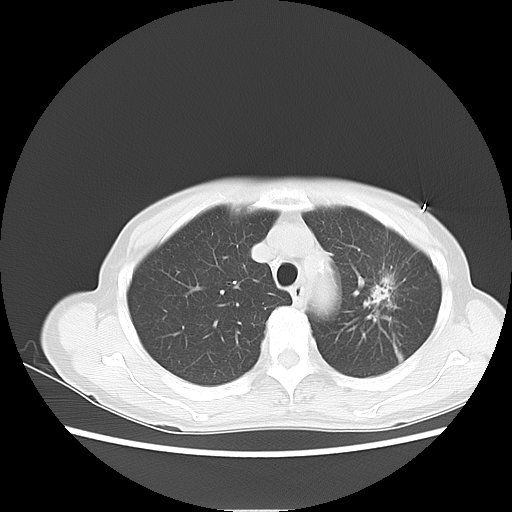
Chest CT, one axial slice; slice 7 of 14 in the series (ordered by position); reconstruction kernel LUNG; 120 kVp; lung window (W 1500 / L -600 HU); 5 mm slice thickness; 512 × 512 image matrix, field of view 350 × 350 mm. Patient: female, 71 years. From the clinical record (not read from this slice): clinical TNM (as recorded): T2 N0 M0.
Outlined on this slice (bounding box drawn by a radiologist):
- lung tumour (recorded histology: adenocarcinoma): bounding box [x1, y1, x2, y2] px = [363, 271, 399, 308]